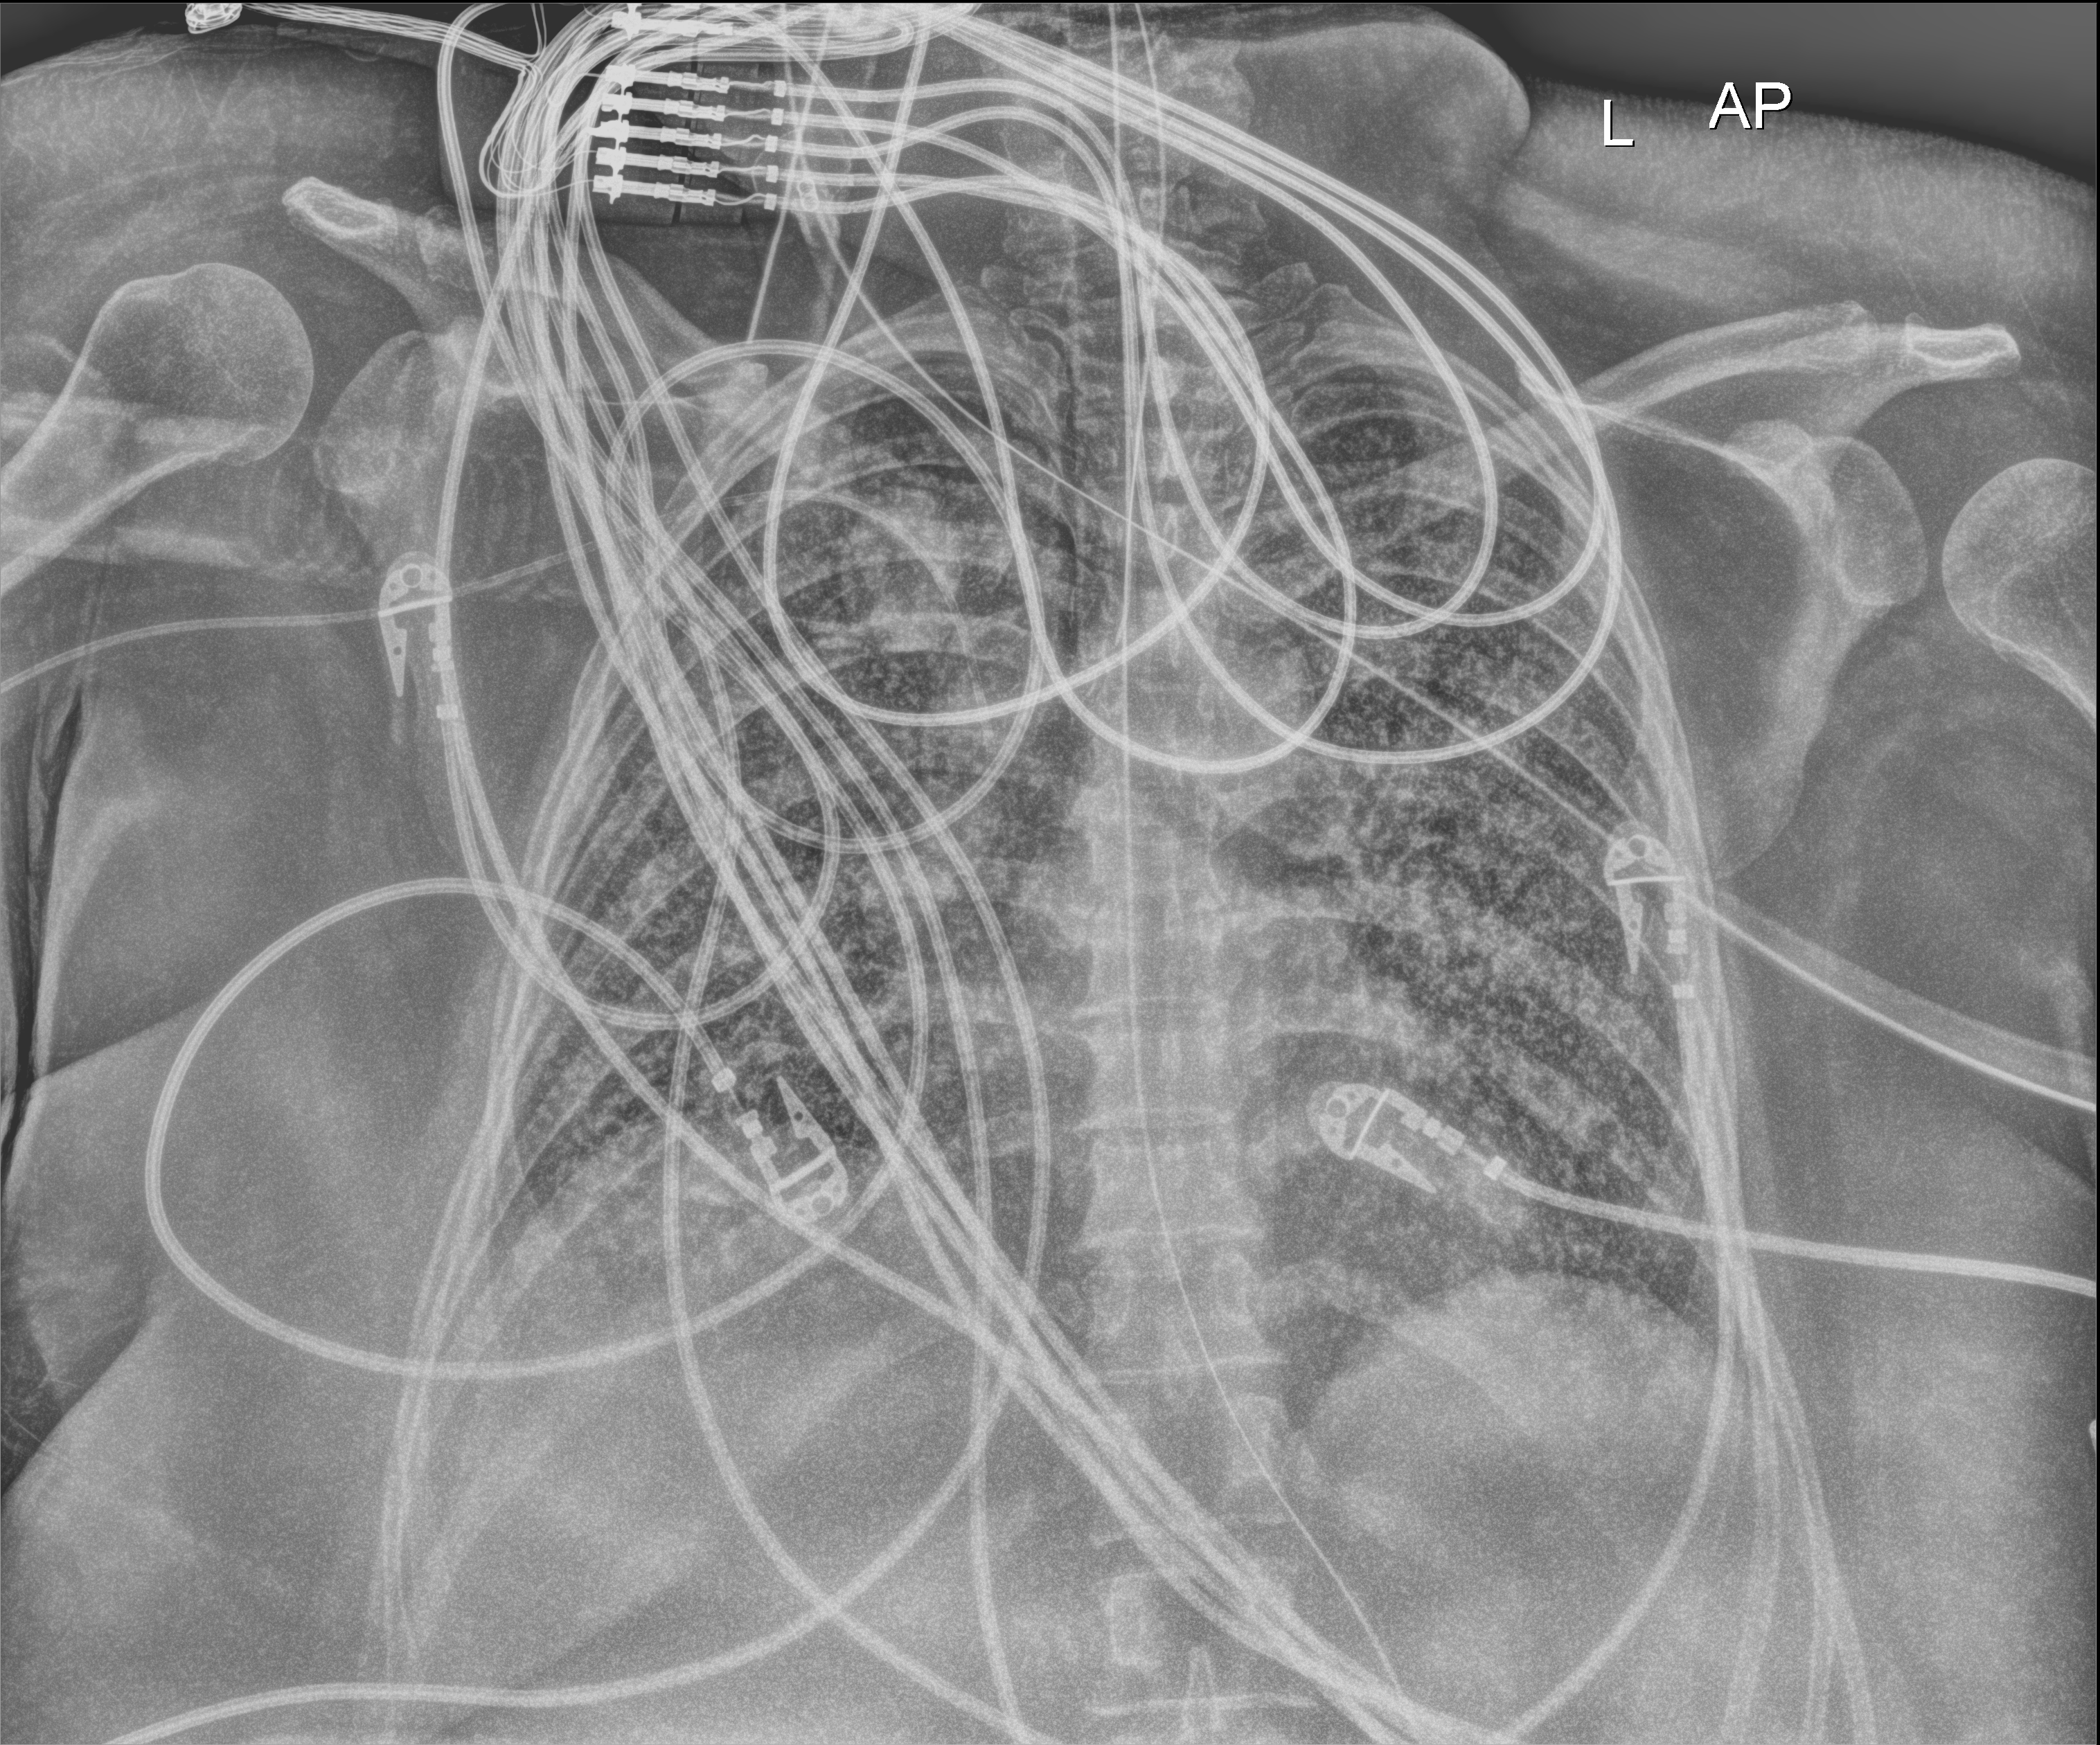
Portable chest radiograph; anteroposterior (AP) projection. Patient hospitalised with COVID-19; female, aged 18–59 years.
Admission-level facts for this patient (not findings on this image; timing relative to this image not recorded): hypertension (admission record): yes.